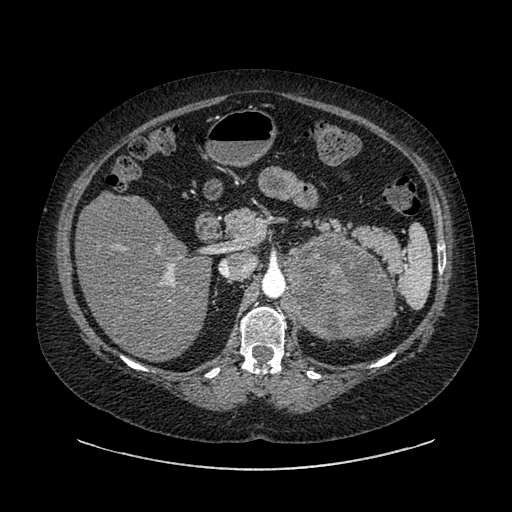
Contrast-enhanced abdominal CT, one axial slice; slice 566 of 769 in the series (ordered by position); intravenous contrast given; soft-tissue window (W 400 / L 40 HU); 0.62 mm slice thickness; 512 × 512 image matrix, field of view 460 × 460 mm. Patient: female, 61 years. From the clinical record (not read from this slice): diagnosis: adrenocortical carcinoma; tumour side: left adrenal; tumour size at pathology: 13 cm; Ki-67 index: 79 %; stage (as recorded): 2.
Annotated regions visible in this slice (semi-automatic segmentation, software-assisted and operator-edited):
- mass: bounding box (x1, y1, x2, y2) in pixels: (282, 231, 392, 341)